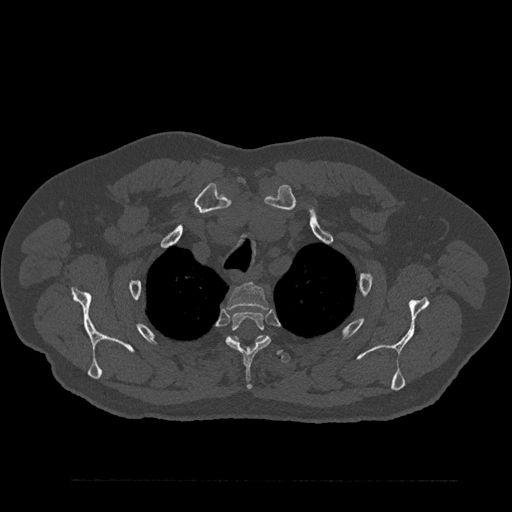
CT including the spine, one axial slice. Position 683 of 797 along the scan axis. Reconstruction kernel Br40s/3. Bone window (W 1800 / L 400 HU). 512 × 512 image matrix. Patient: male, 61 years. From the clinical record (not read from this slice): primary cancer: prostate.
Outlined on this slice (semi-automatically segmented with operator editing):
- T2 vertebra: bounding box <227,283,268,309> (left, top, right, bottom; pixels)
- T3 vertebra: <225,311,271,390>
- T4 vertebra: <216,336,290,363>